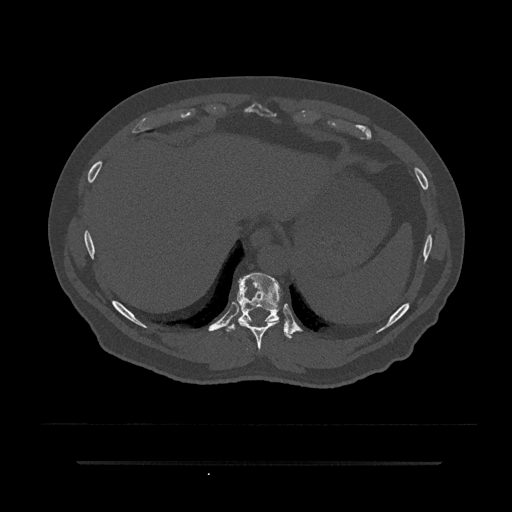
CT including the spine, one axial slice. Reconstruction kernel Br40s/3. Bone window (W 1800 / L 400 HU). 0.5 mm slice thickness. 512 × 512 image matrix, field of view 464 × 464 mm. Male patient, age 59 years. Case-level facts recorded for this patient, not image findings: primary cancer: bile ducts; vertebrae with lytic lesions (as recorded): T10.
Outlined on this slice (semi-automatically segmented with operator editing):
- T10 vertebra: box from (x=226, y=273) to (x=292, y=338) px
- T9 vertebra: (x=241, y=323)–(x=275, y=350)